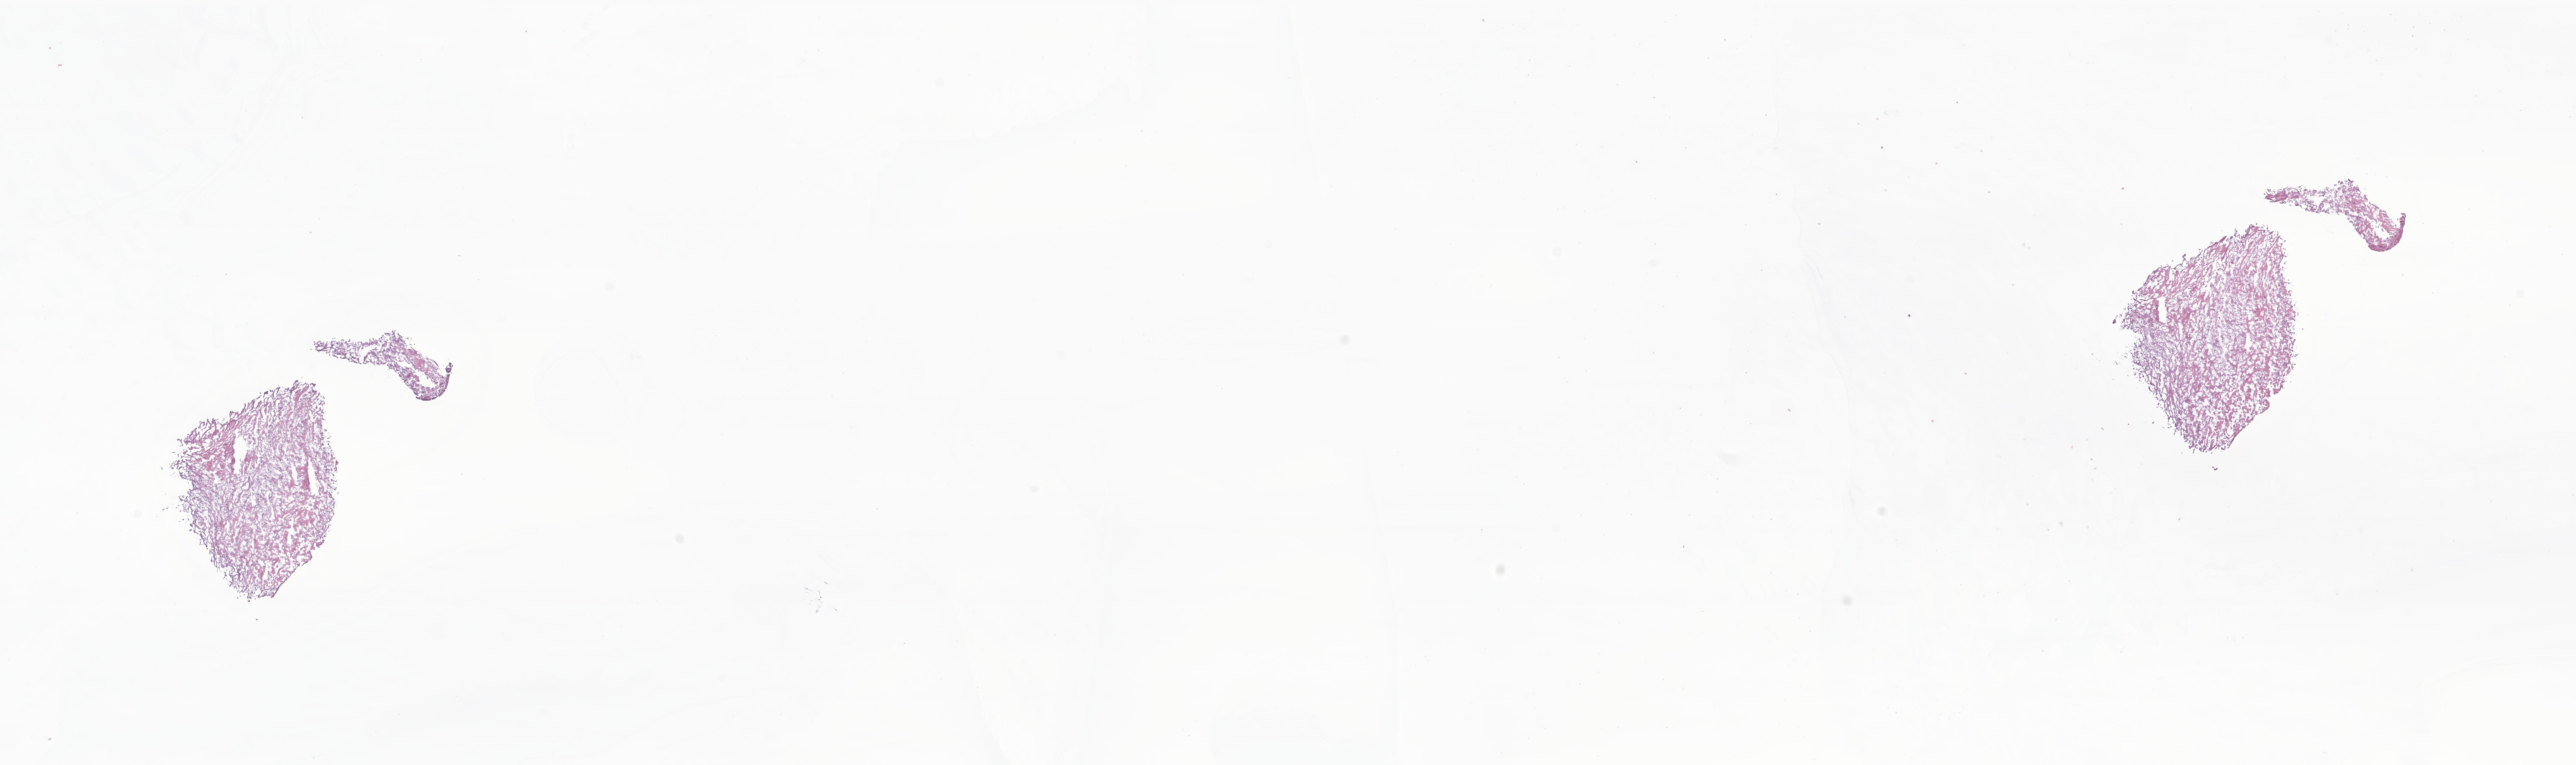
Digitized haematoxylin and eosin-stained section of tumor tissue from the brain — a low-resolution overview of the entire scanned area, about 29.1 x 8.6 mm. Frozen section (OCT-embedded). Patient: female, age 216 months (18 years).
- recorded diagnosis: Clear cell meningioma